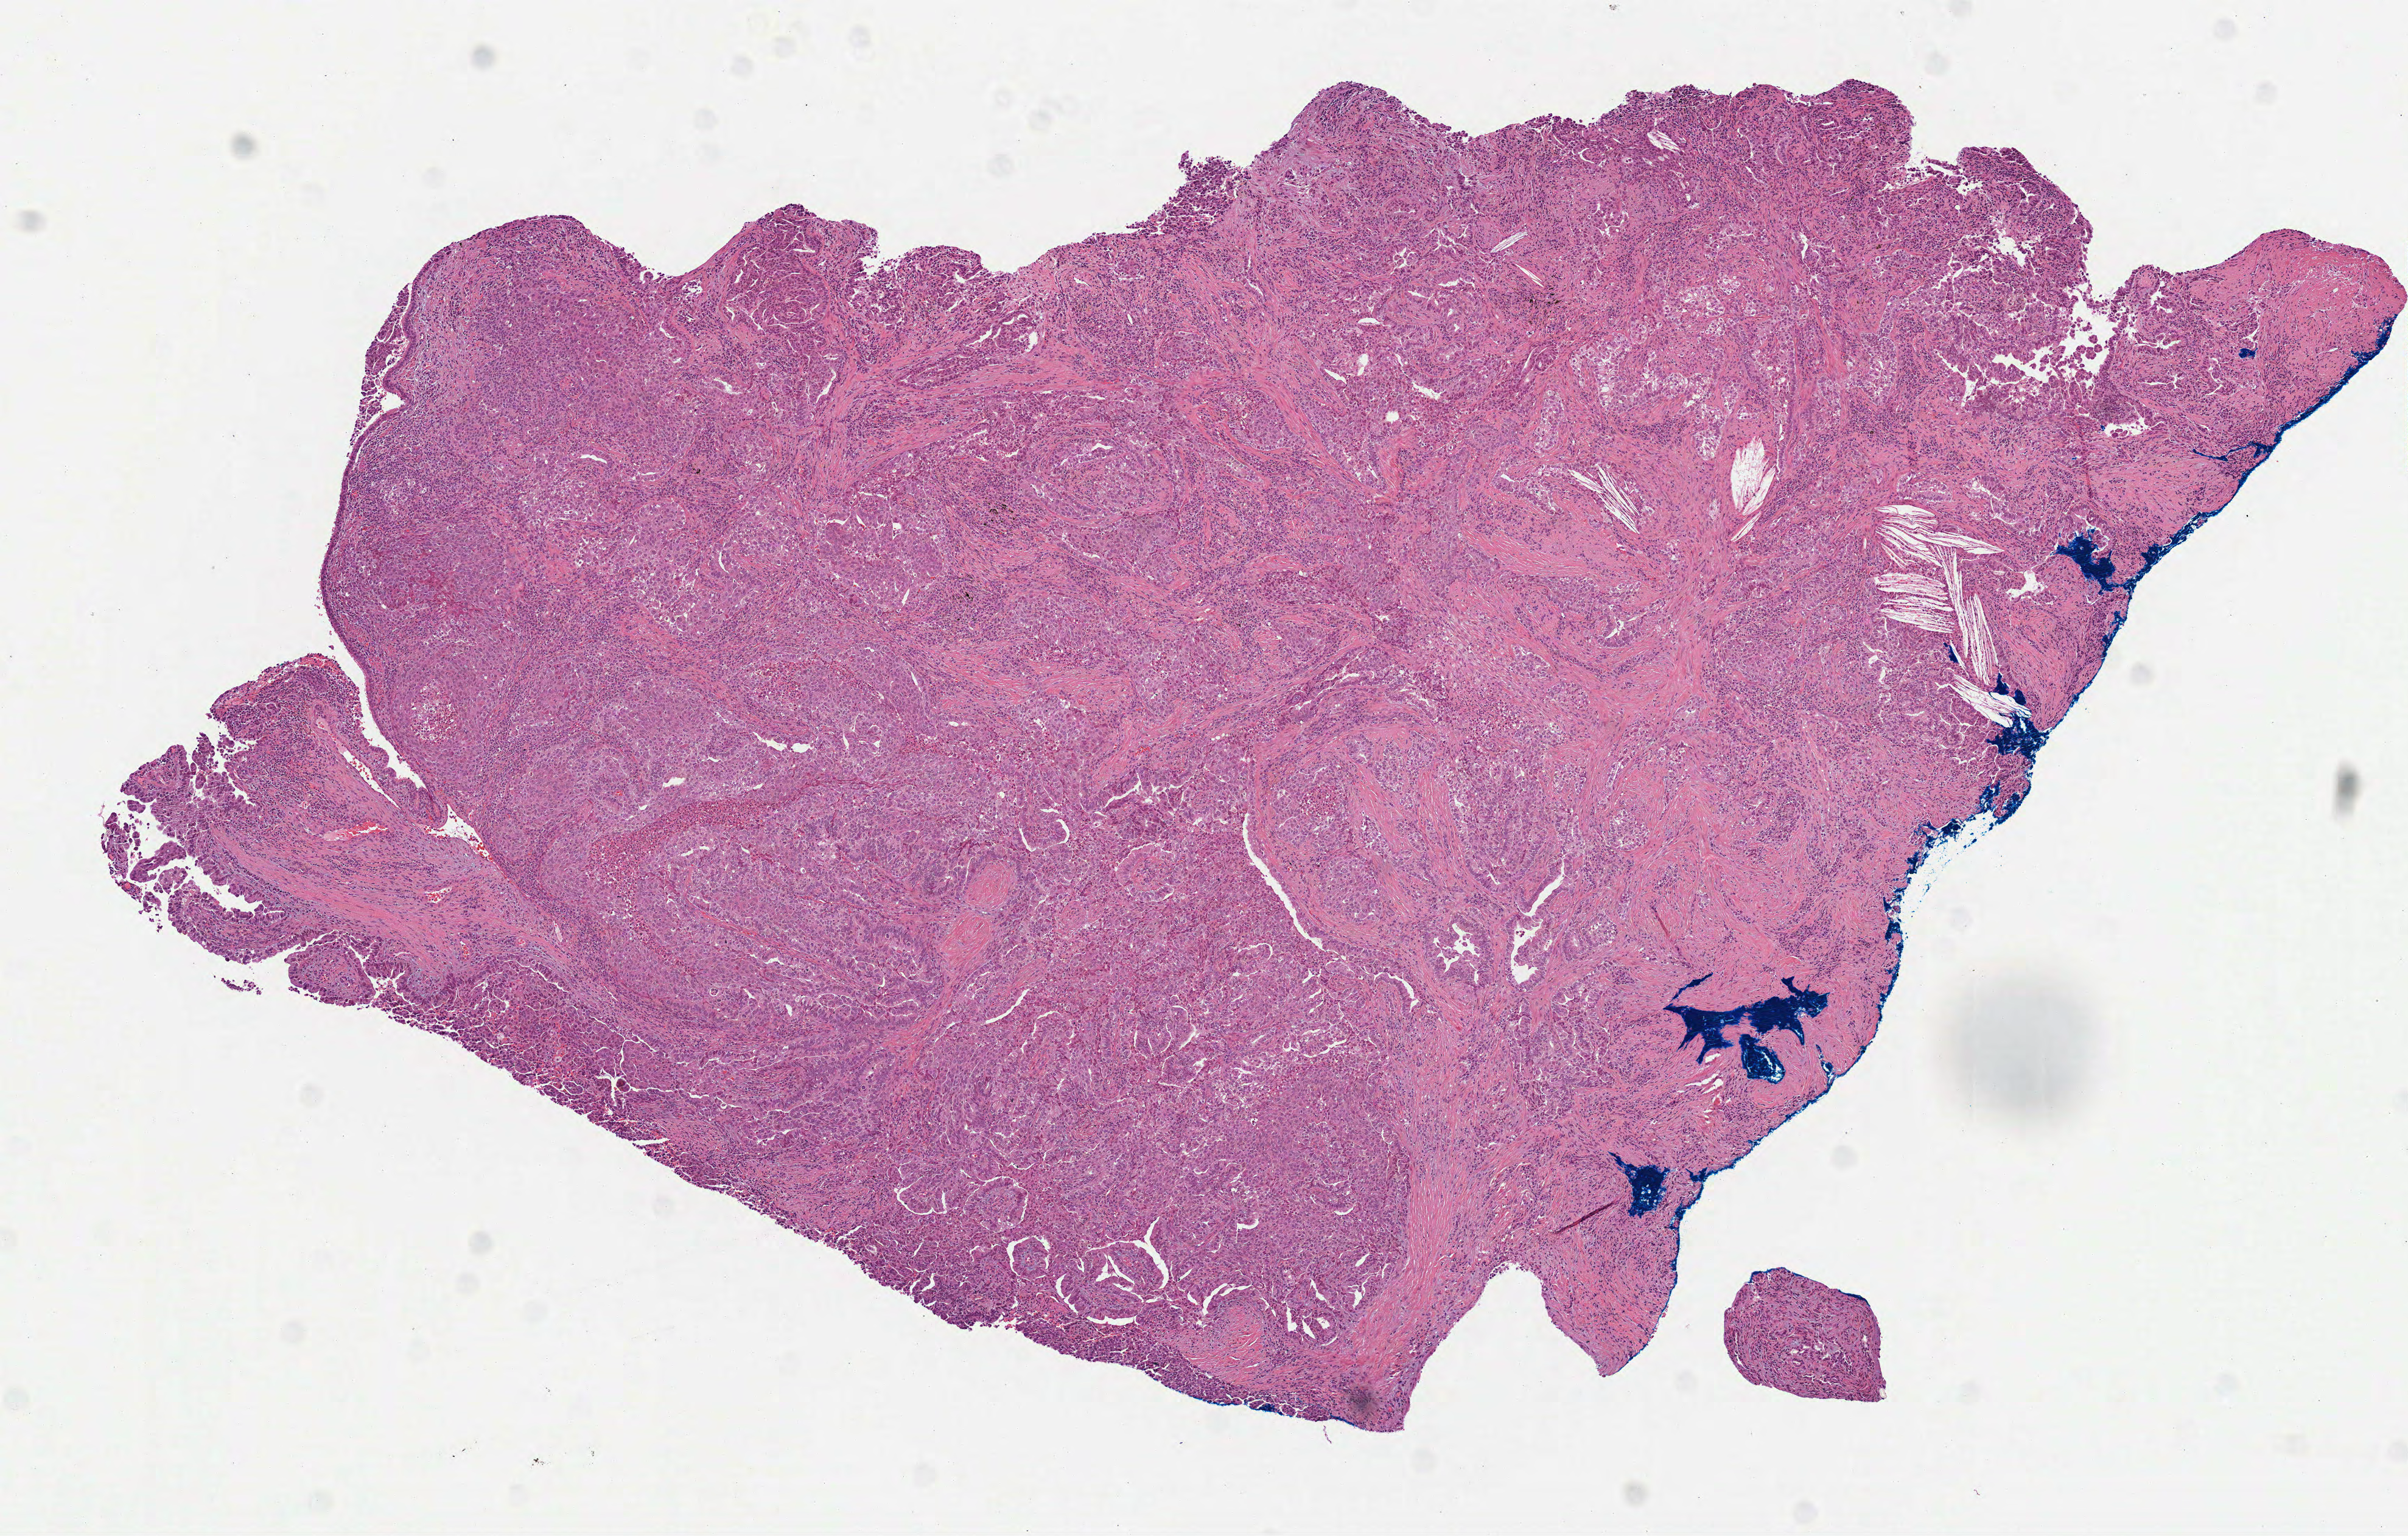
Digitized H&E-stained tissue section (whole slide), a low-resolution overview of the entire scanned area, about 8.0 x 5.1 mm (from a 40x scan); formalin-fixed paraffin-embedded (FFPE) diagnostic section; lung, primary tumour sample. Male, age 64 years at initial diagnosis.
AJCC pathologic stage: IA (7th edition). Pathologic diagnosis: Papillary adenocarcinoma, NOS (lower lobe, lung). TNM: T1b N0 M0.